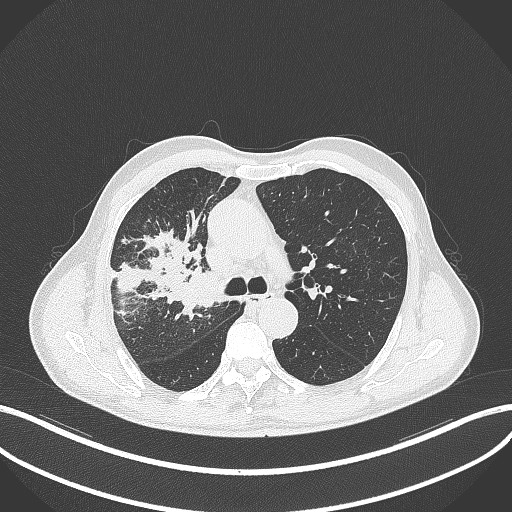
Chest CT, one axial slice; 120 kVp; lung window (W 1500 / L -600 HU); 1 mm slice thickness; 512 × 512 image matrix, field of view 400 × 400 mm. Male patient, age 69 years. From the clinical record (not read from this slice): clinical TNM (as recorded): T2a N0 M0.
Structures marked on this image (bounding box drawn by a radiologist):
- lung tumour (recorded histology: adenocarcinoma): bounding box <176,264,220,314> (left, top, right, bottom; pixels)